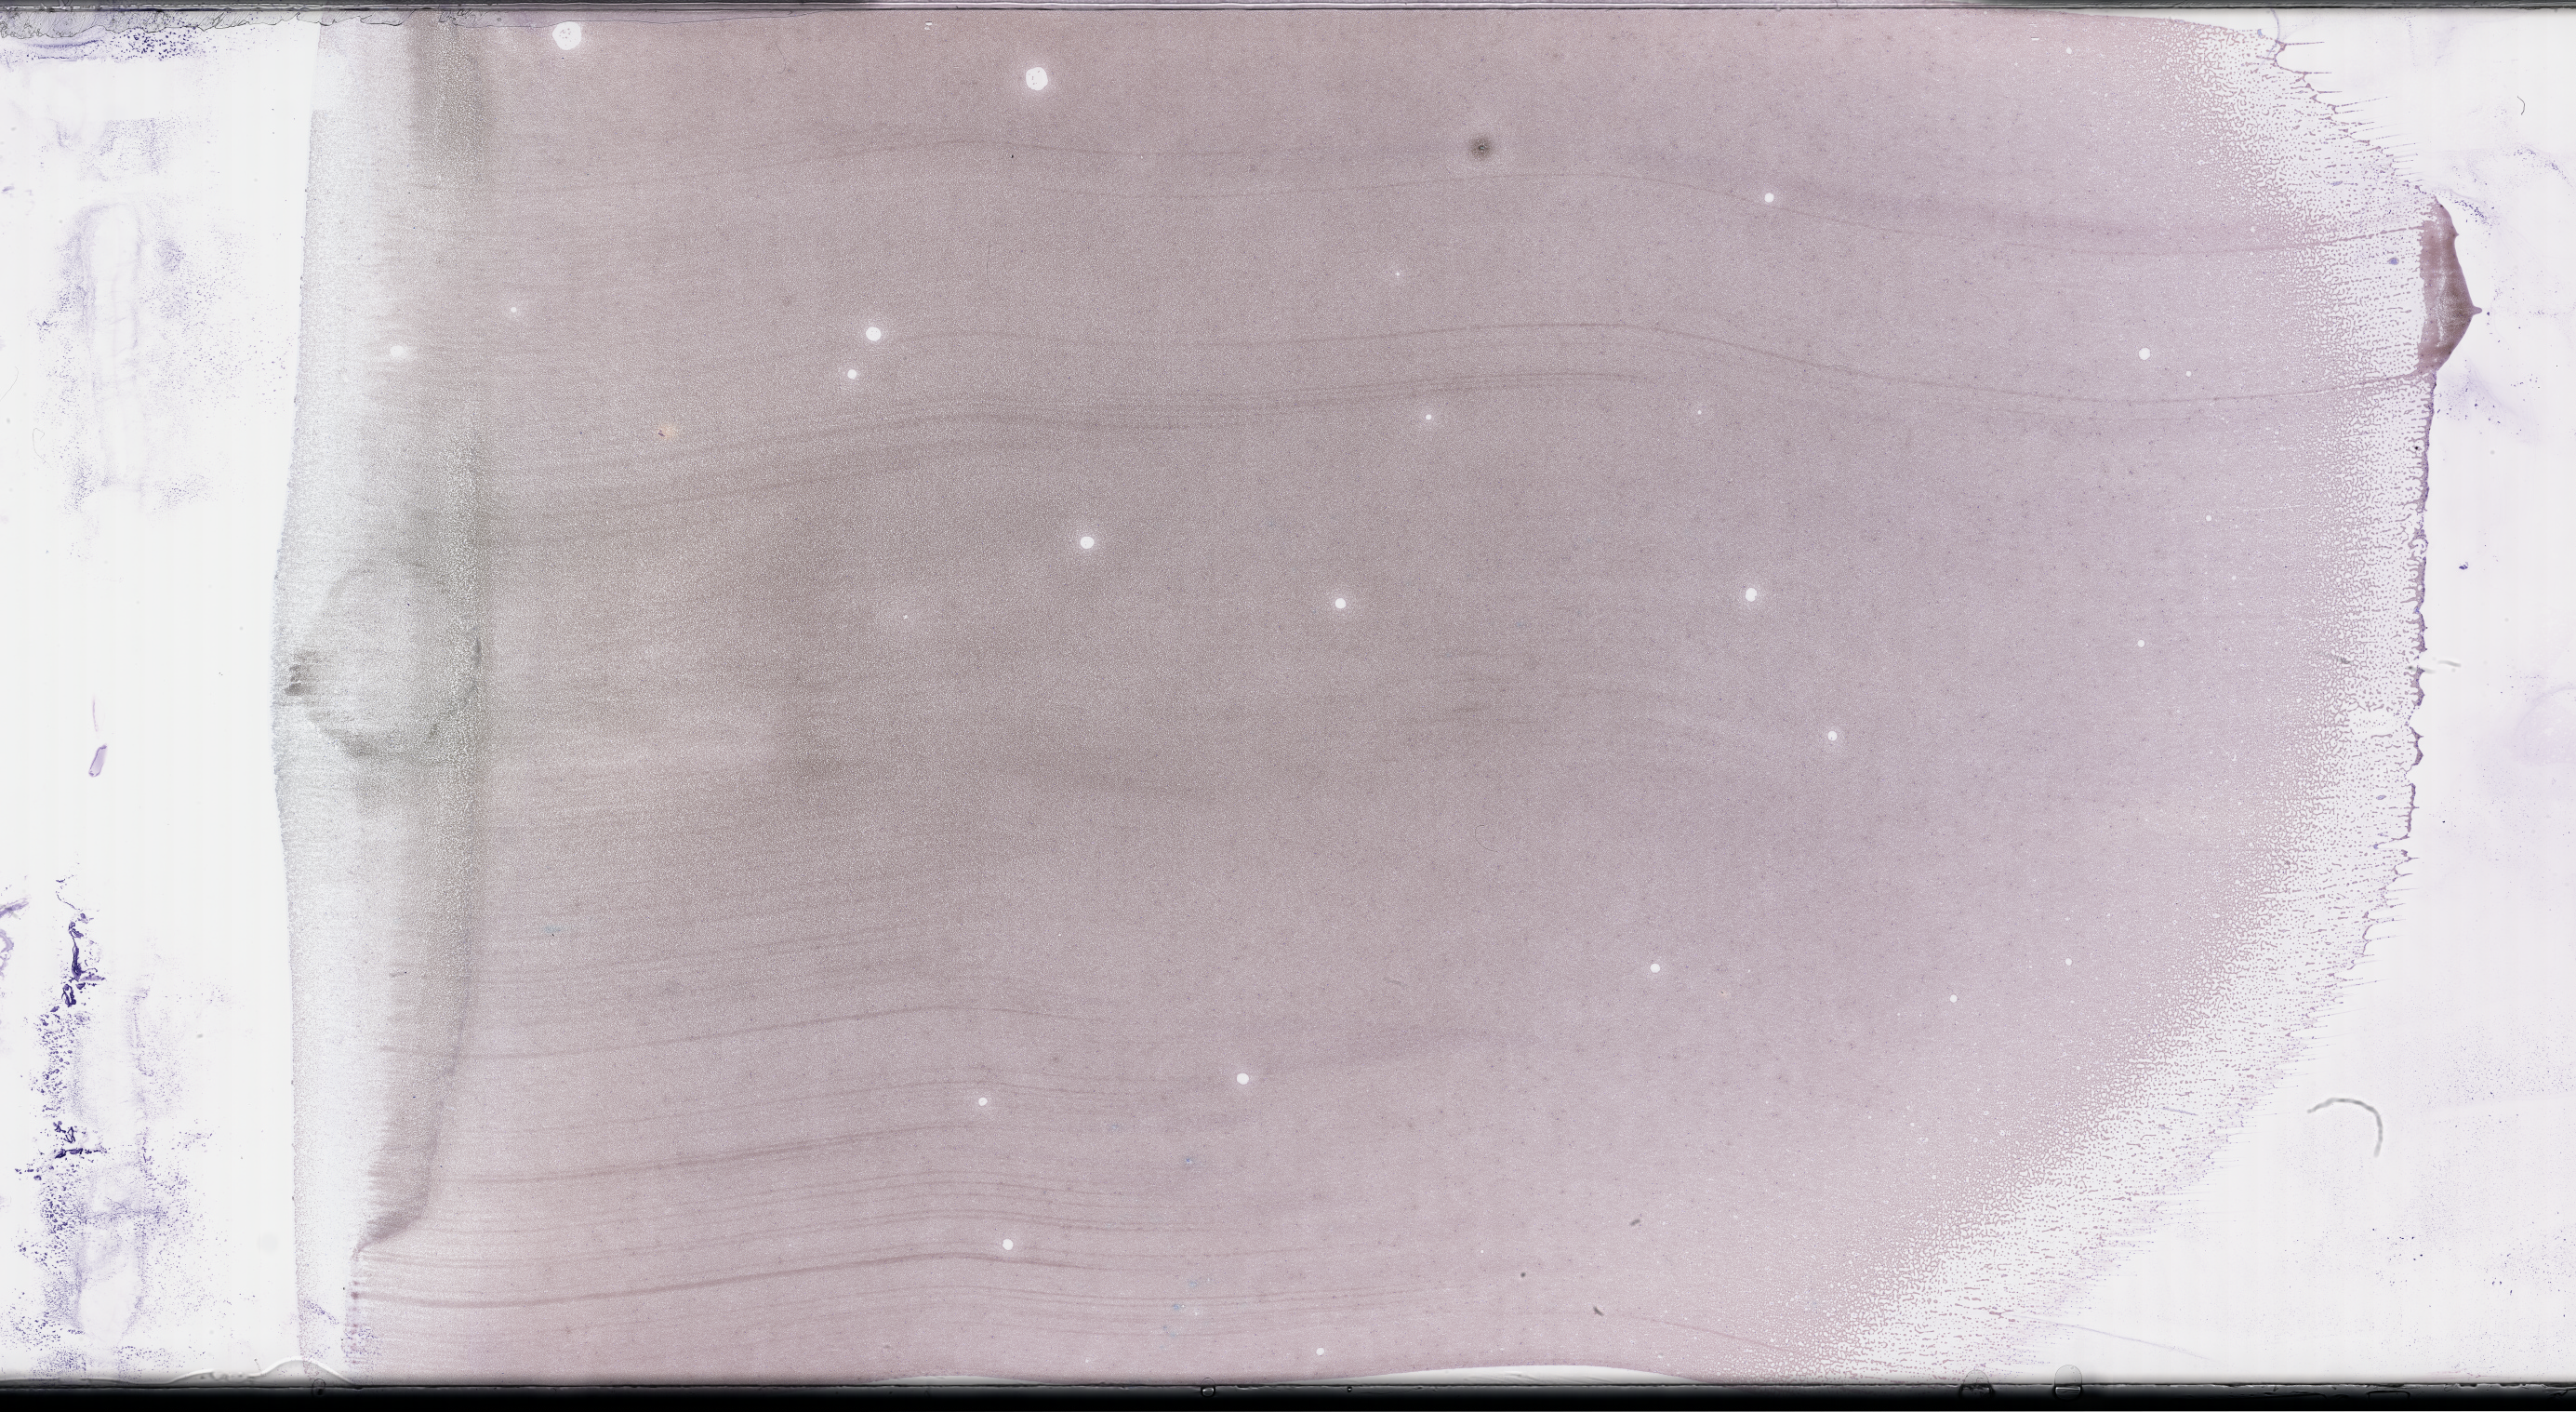
Whole-slide image of a whole blood smear, Wright–Giemsa stain, shown as a low-resolution overview of the whole scanned area (about 44.7 x 24.5 mm). EDTA-anticoagulated smear. Patient: male.
Patient diagnosis: Plasma Cell Myeloma.